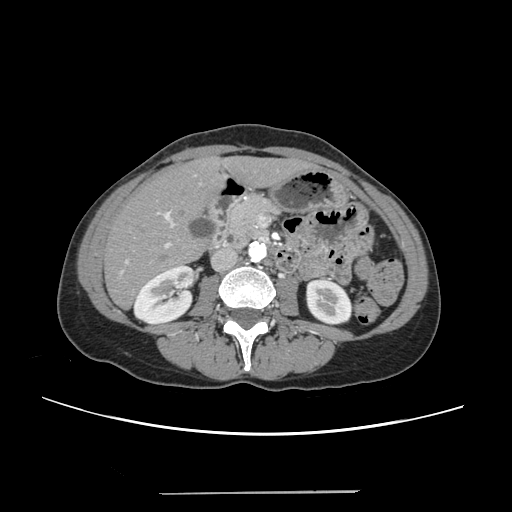
Contrast-enhanced abdominal CT, one axial slice. Position 97 of 240 along the scan axis. 120 kVp. Intravenous contrast given. Soft-tissue window (W 400 / L 40 HU). 1.25 mm slice thickness. 512 × 512 image matrix. Female patient, age 60 years. Case-level facts recorded for this patient, not image findings: diagnosis: colorectal cancer liver metastases, imaged before liver resection; multiple liver metastases: no; largest metastasis: 1.5 cm; chemotherapy before resection: yes.
Annotated regions visible in this slice (expert manual segmentation):
- liver: box from (x=106, y=158) to (x=304, y=308) px
- planned liver remnant (the part of the liver to remain after resection): (x=106, y=160)–(x=304, y=308)
- portal vein (with intrahepatic branches): (x=121, y=174)–(x=196, y=273)